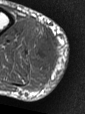
MRI of an extremity soft-tissue mass, one axial slice. Position 13 of 47 along the scan axis. MR volume resampled by the dataset authors to the PET/CT grid (not the native acquisition matrix). 85 × 114 image matrix, field of view 83 × 111 mm. Male patient. From the clinical record (not read from this slice): histological type: pleiomorphic liposarcoma; grade: high; site of the primary tumour: right calf.
Structures marked on this image (expert contour drawn on MRI and transferred to this co-registered scan by the dataset authors):
- gross tumour volume including surrounding oedema: box from (x=27, y=30) to (x=57, y=85) px
- gross tumour volume (mass): (x=33, y=39)–(x=50, y=58)